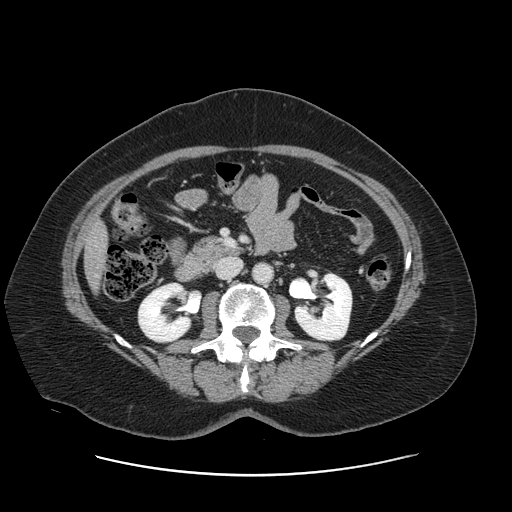
Contrast-enhanced abdominal CT, one axial slice. Position 47 of 161 along the scan axis. 120 kVp. Intravenous contrast given. Soft-tissue window (W 400 / L 40 HU). 2.5 mm slice thickness. 512 × 512 image matrix, field of view 398 × 398 mm. Female patient, age 62 years. From the clinical record (not read from this slice): diagnosis: colorectal cancer liver metastases, imaged before liver resection; multiple liver metastases: no; largest metastasis: 2.5 cm; chemotherapy before resection: yes.
Outlined on this slice (expert manual segmentation):
- liver: bounding box <87,225,107,288> (left, top, right, bottom; pixels)